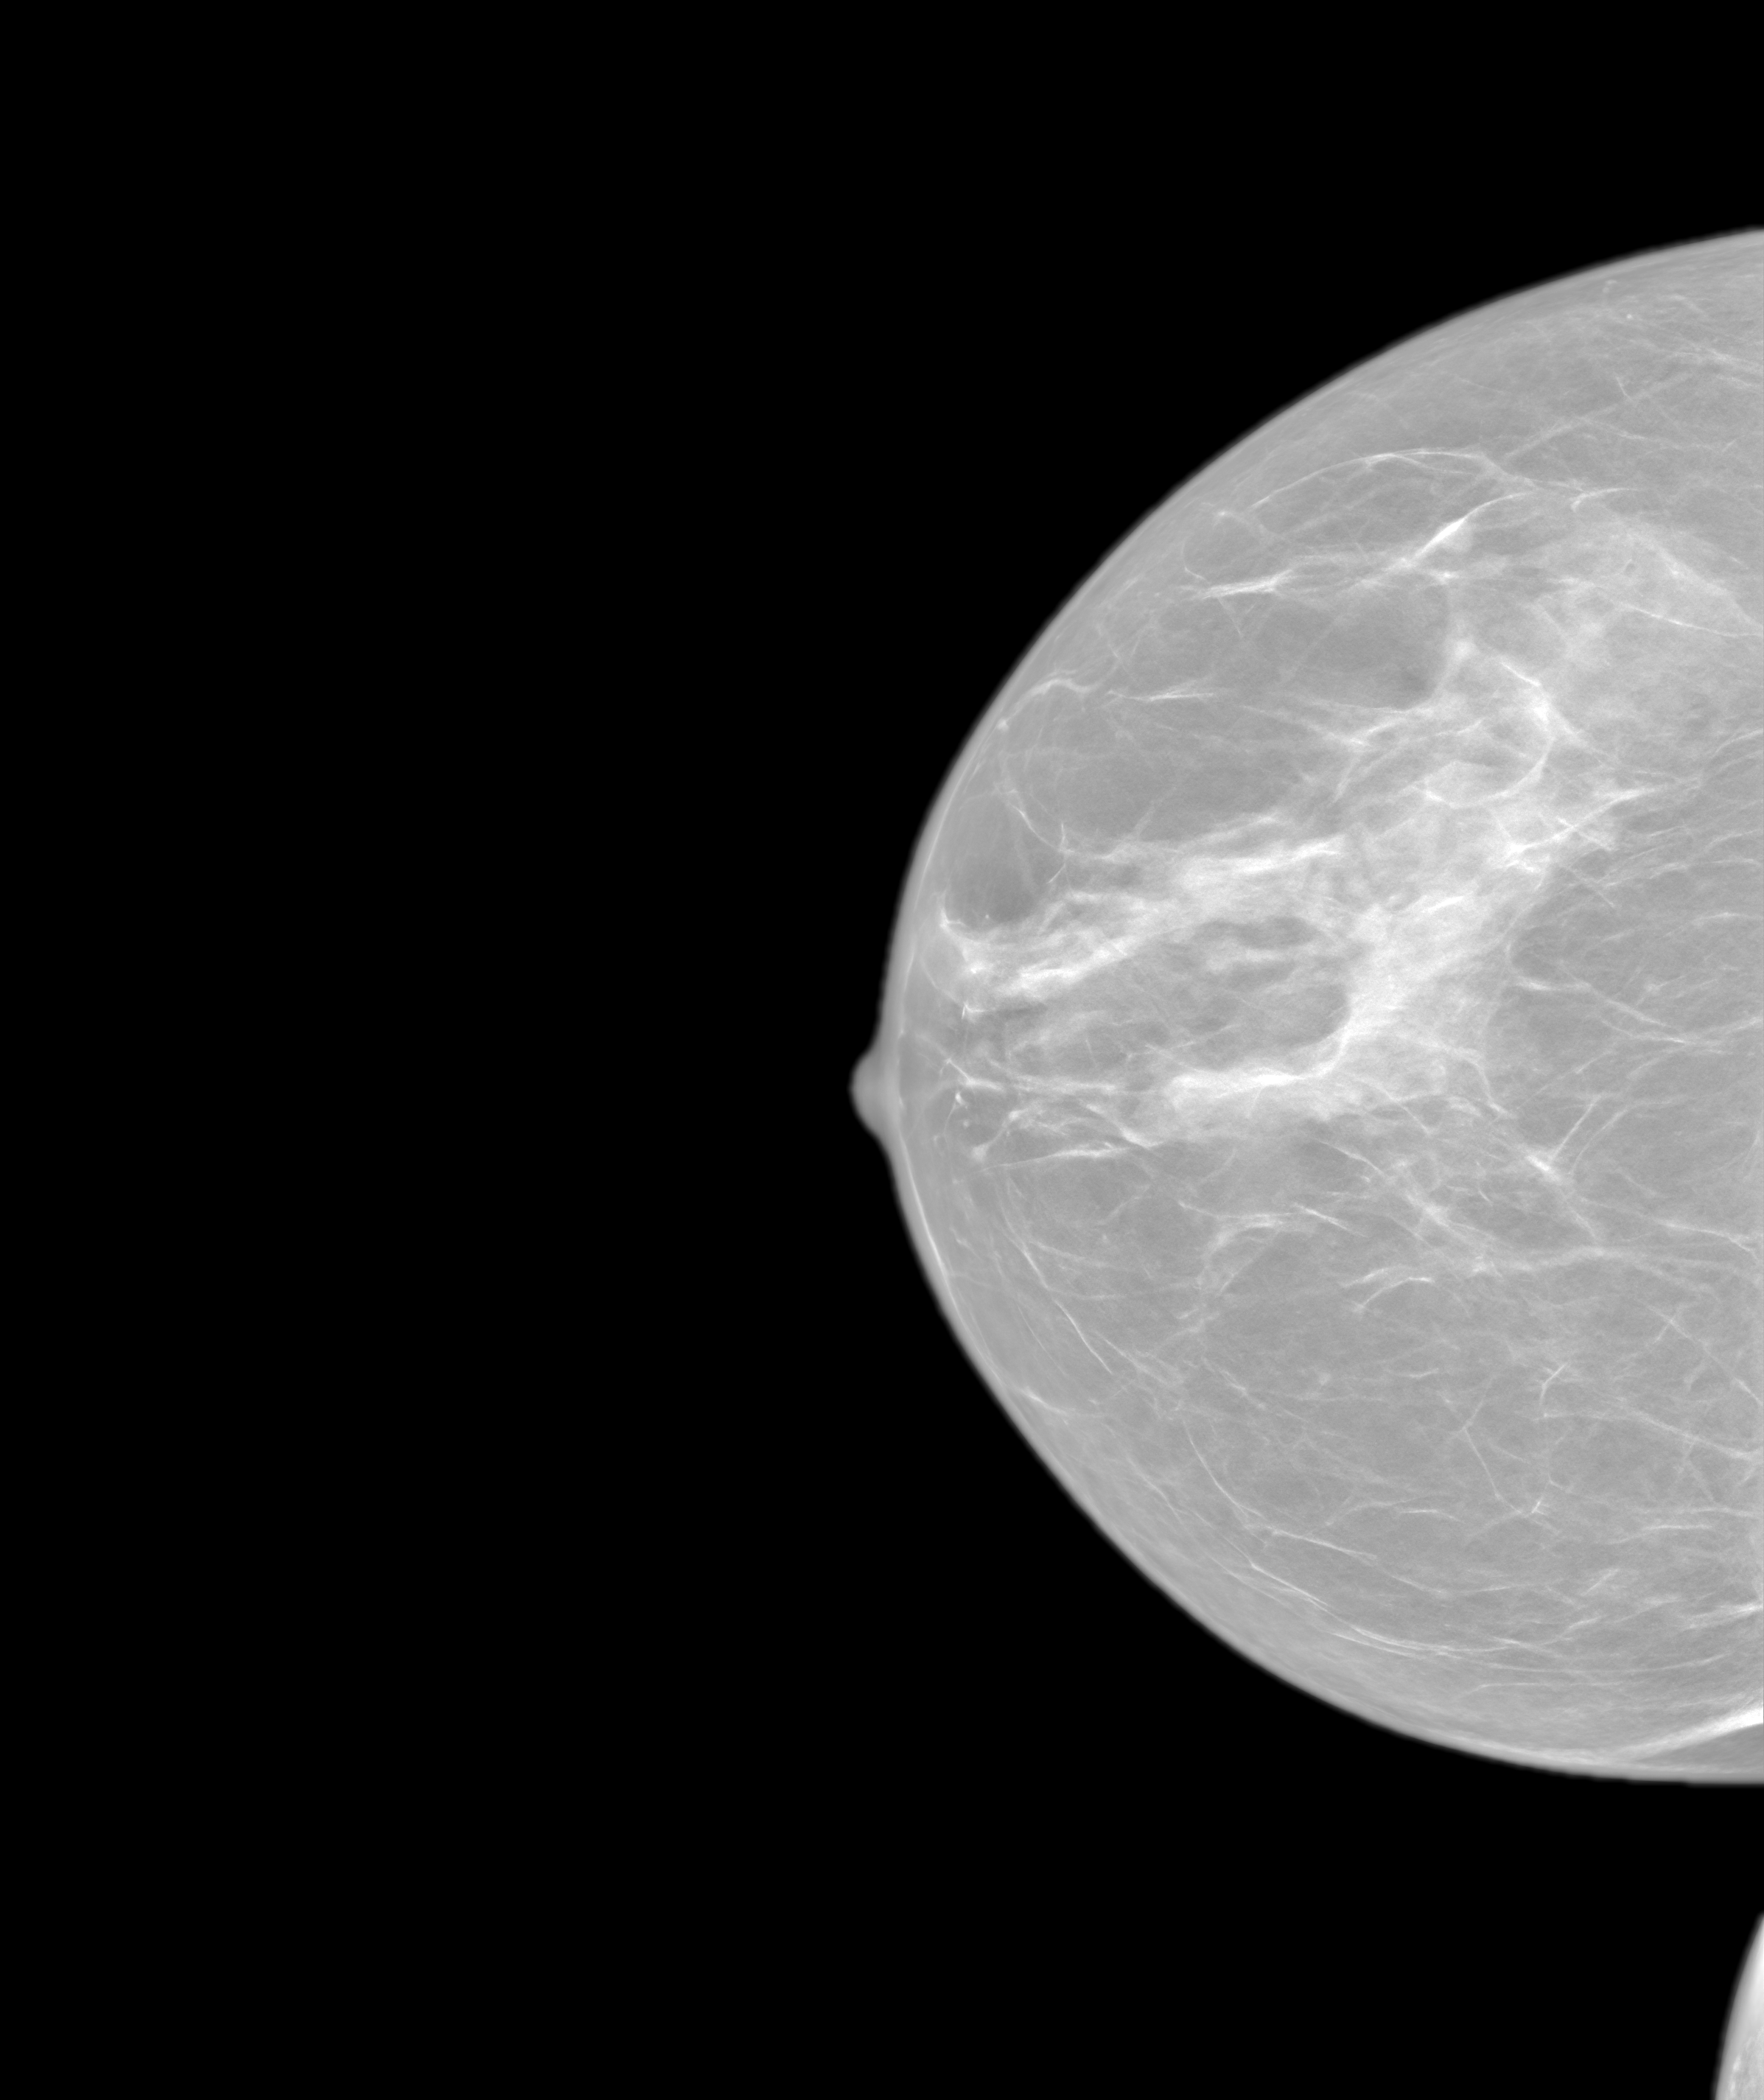
Synthetic 2-D view generated from a tomosynthesis acquisition (not an FFDM exposure), right breast, craniocaudal (CC) view, annual screening mammography examination. Patient: female, 56 years.
Breast density at the screening exam (both breasts): heterogeneously dense (BI-RADS density category c). Final BI-RADS category for the screening round (tomosynthesis exam, both breasts): category 1. Recall: no recall after this screen.